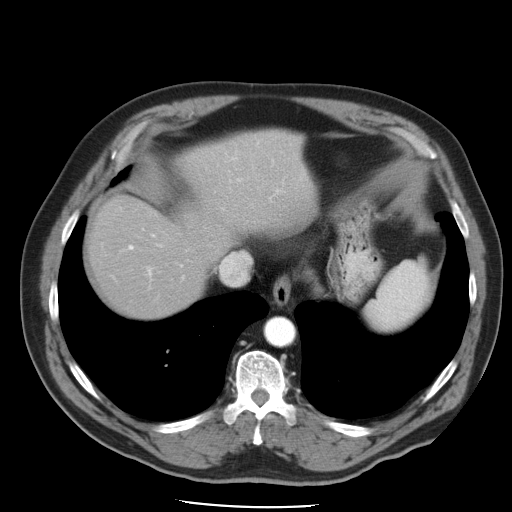
Contrast-enhanced abdominal CT, one axial slice. Slice 41 of 49 in the series (ordered by position). Reconstruction kernel STANDARD. 120 kVp. Intravenous contrast given. Soft-tissue window (W 400 / L 40 HU). 5 mm slice thickness. 512 × 512 image matrix, field of view 395 × 395 mm. Male patient, age 68 years. Case-level facts recorded for this patient, not image findings: diagnosis: colorectal cancer liver metastases, imaged before liver resection; multiple liver metastases: yes; largest metastasis: 1.7 cm; disease in both lobes: no.
Outlined on this slice (expert manual segmentation):
- hepatic veins: box from (x=220, y=208) to (x=249, y=285) px
- liver: (x=91, y=134)–(x=309, y=318)
- planned liver remnant (the part of the liver to remain after resection): (x=91, y=133)–(x=306, y=318)
- portal vein (with intrahepatic branches): (x=130, y=155)–(x=279, y=279)